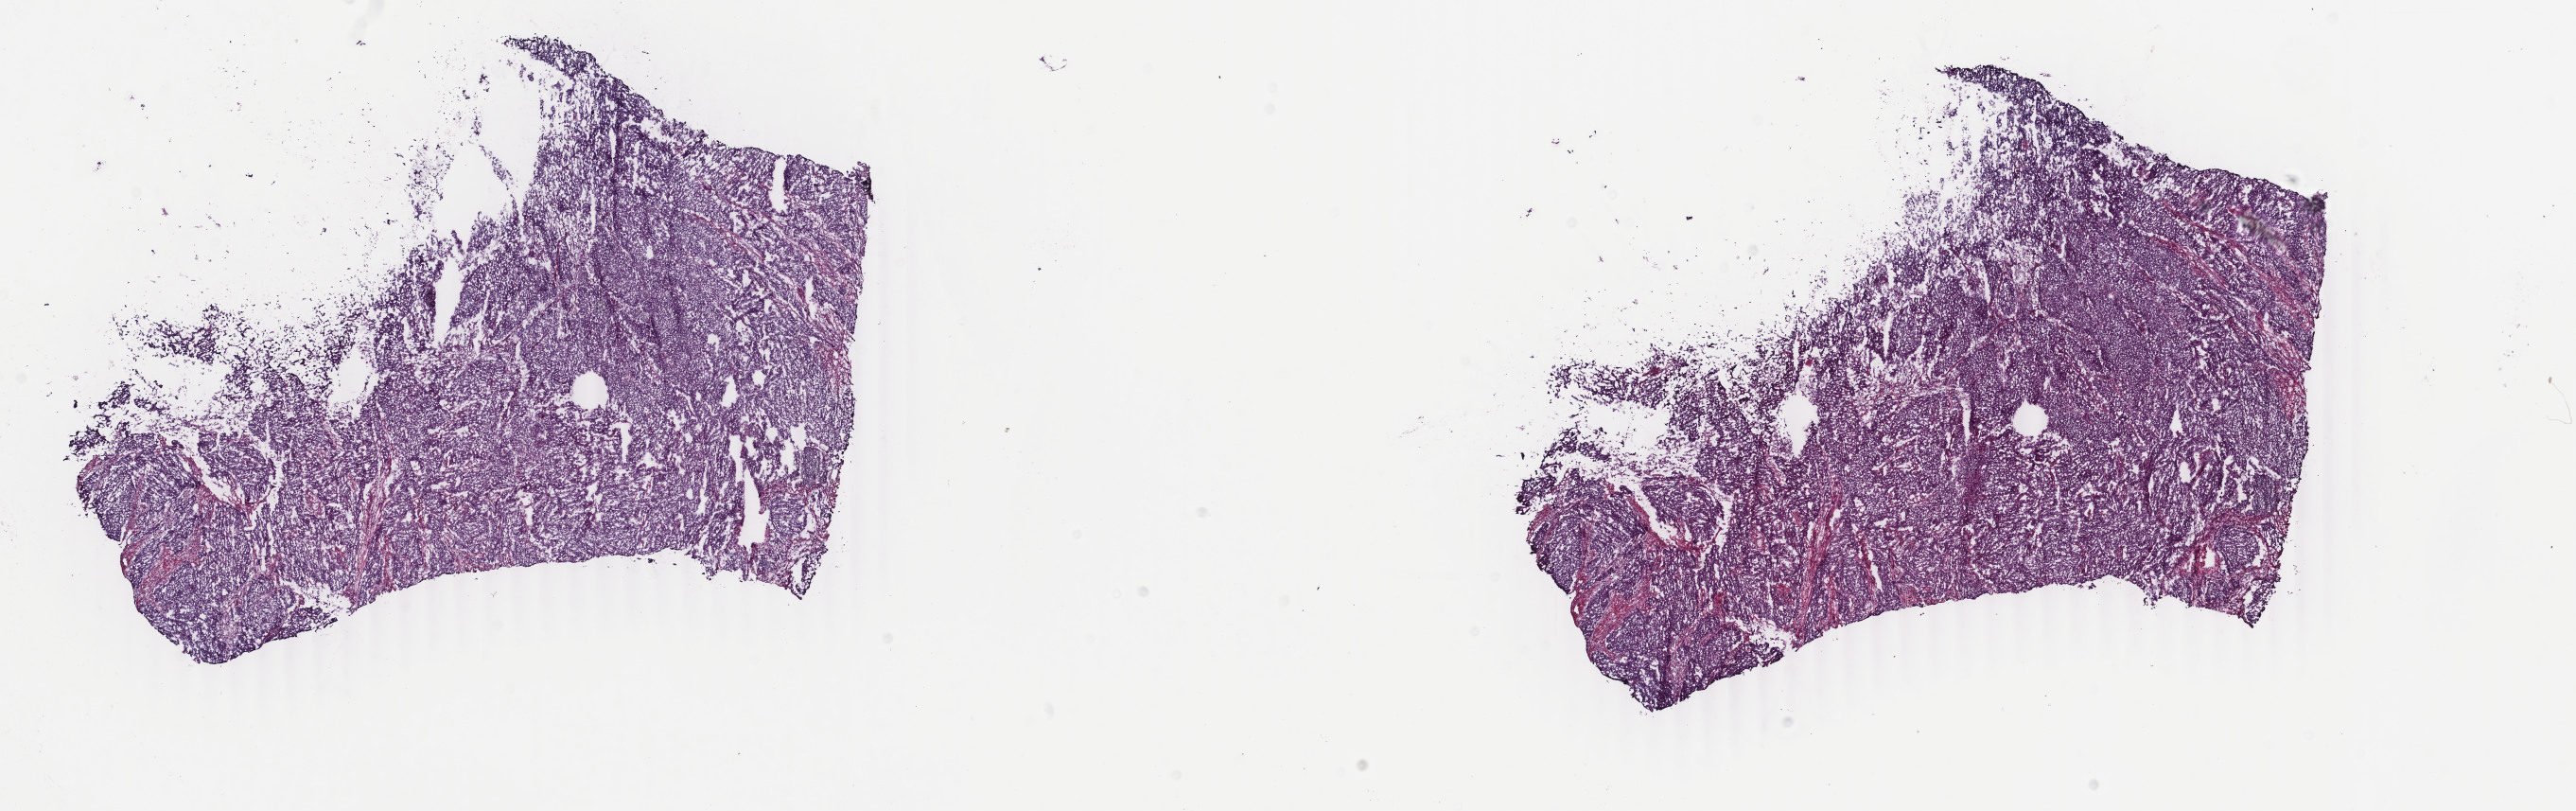
Whole-slide histology image, H&E-stained, a low-resolution overview of the entire scanned area, about 21.7 x 6.8 mm; frozen section; sample: primary tumour, uterus. Patient: female, age at initial diagnosis 56 years. Histologic grade: G3 (poorly differentiated). Pathologist review of this section (percent, as recorded): tumour cells 80%, tumour nuclei 80%, normal cells 0%, stromal cells 15%, necrosis 5%. Inflammatory infiltration, as recorded: lymphocyte infiltration 40%, monocyte infiltration 20%, neutrophil infiltration 20%.
• FIGO stage: IB
• lymph nodes positive (case pathology): 0 of 18 examined
• diagnosis: Endometrioid adenocarcinoma, NOS (endometrium)